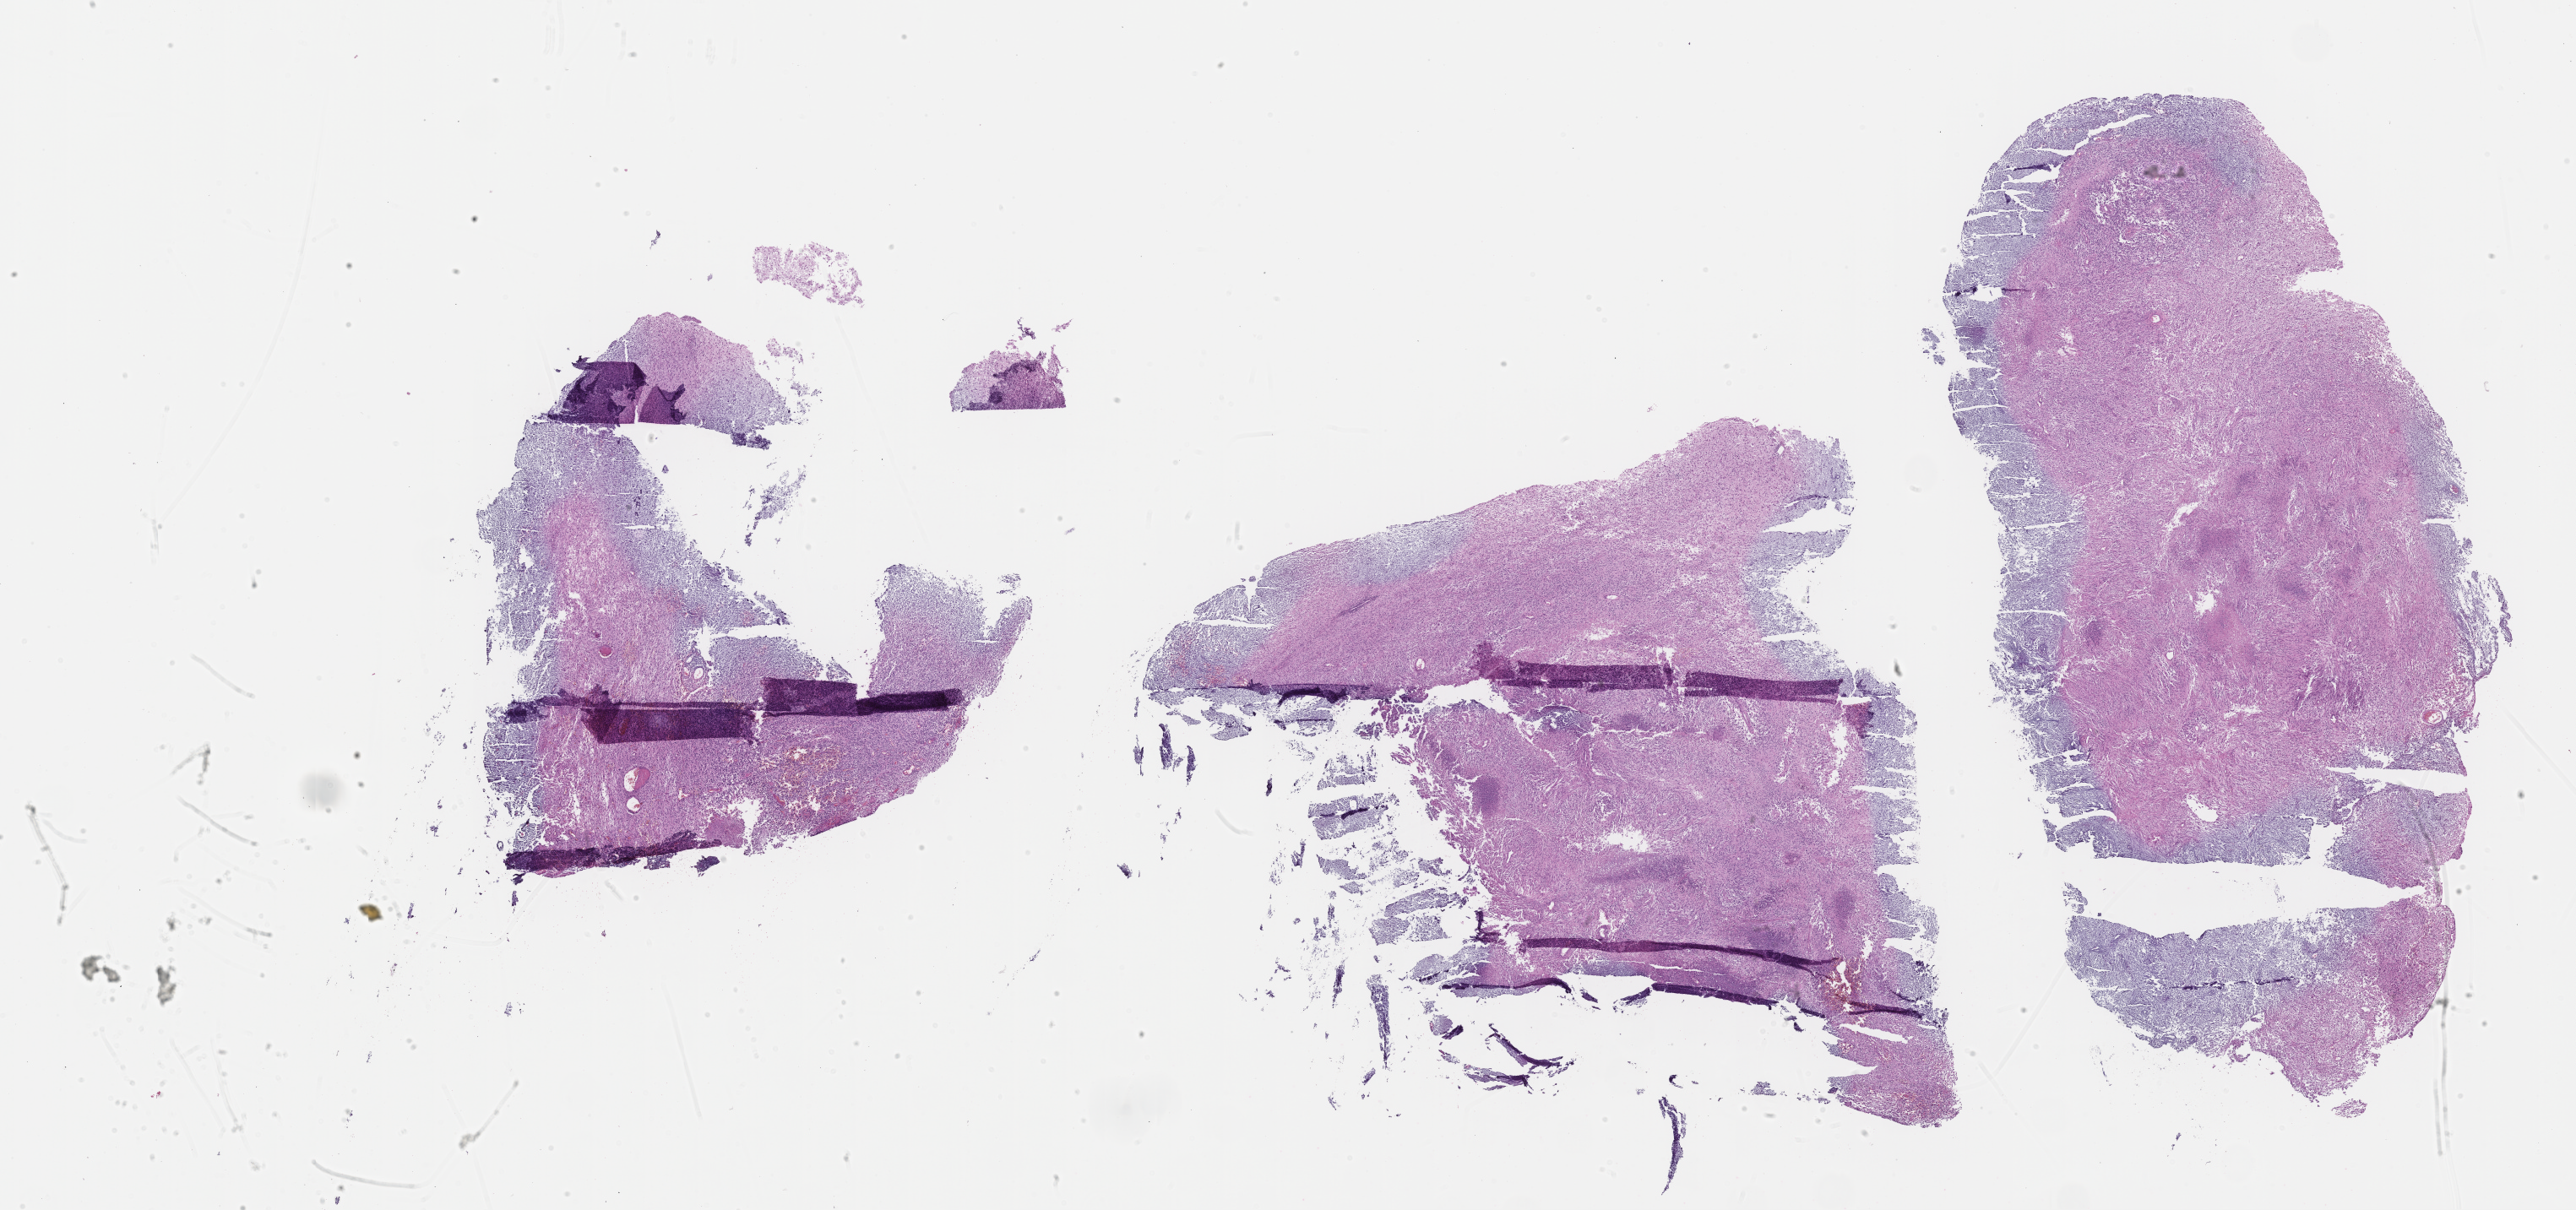
H&E-stained whole-slide image, whole scanned area (about 24.7 x 11.6 mm, from a 40x scan) shown as a low-resolution overview; FFPE section; brain, primary tumour sample. Patient: male, age at initial diagnosis 74 years.
Histologic diagnosis: Glioblastoma.